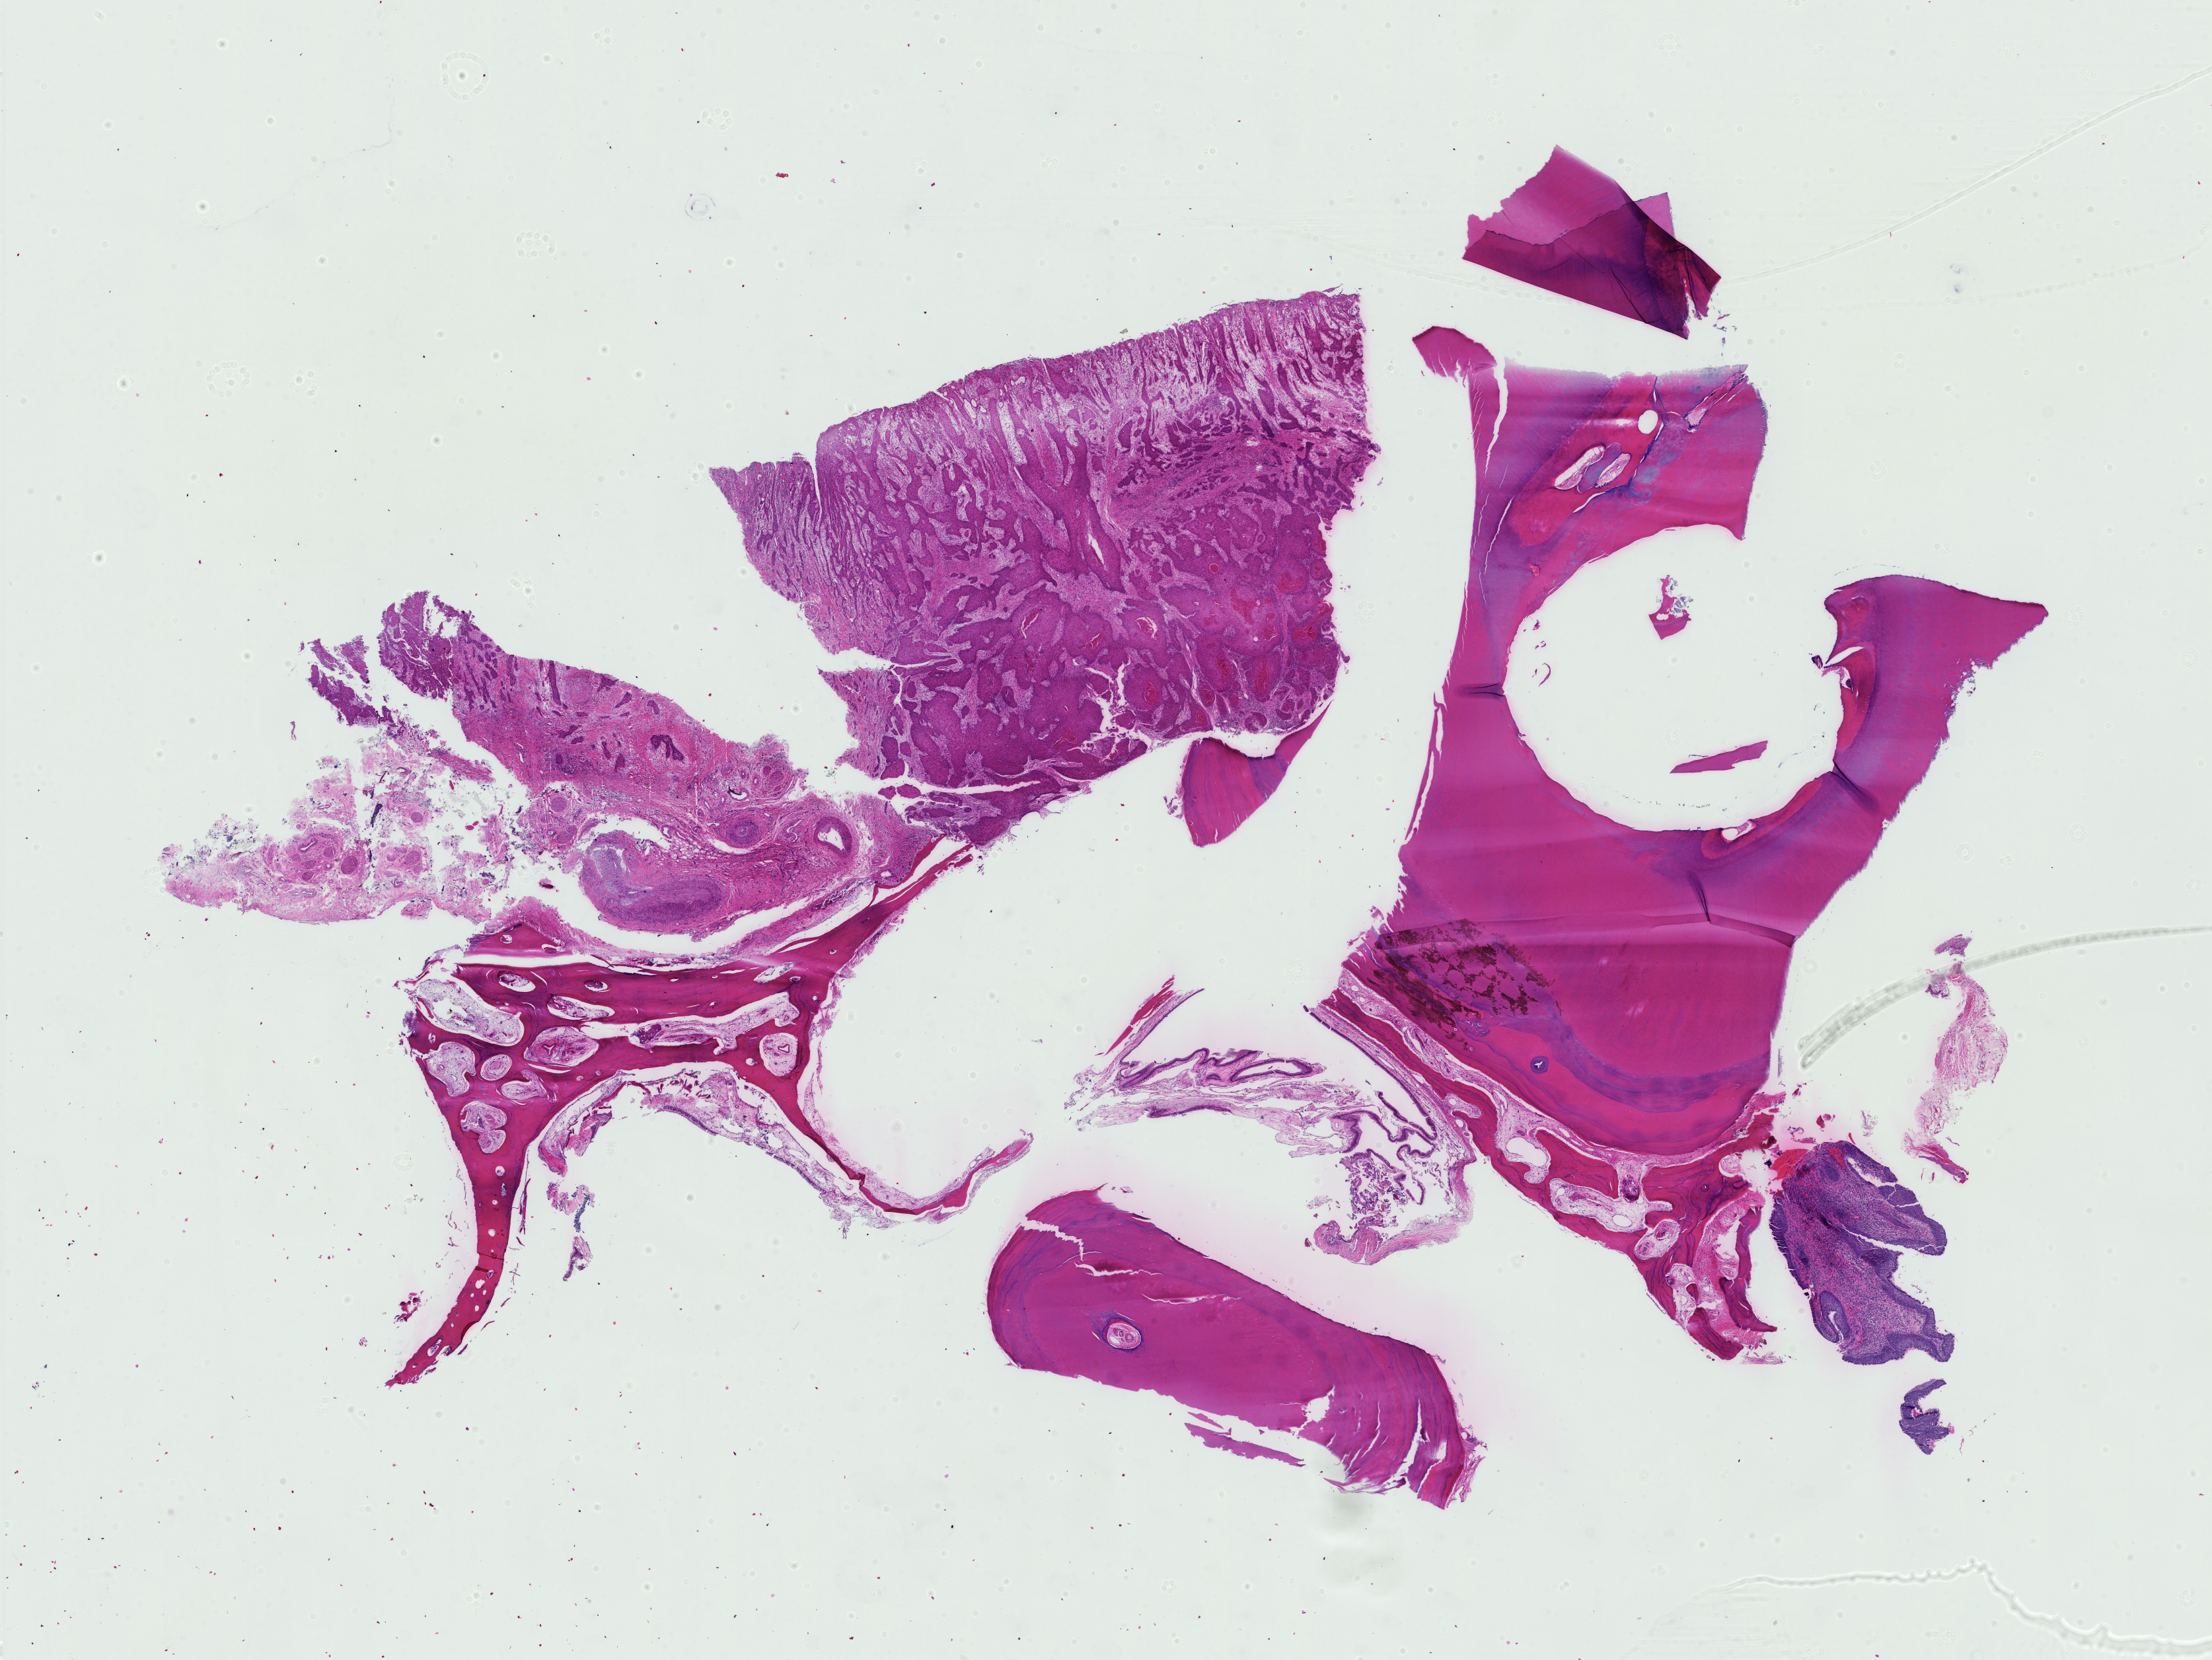
Digitized Hematoxylin and eosin (H&E) stained tissue section (whole slide) — low-resolution overview of the scanned area, about 24.3 x 18.2 mm (acquisition: 40x scan), formalin-fixed paraffin-embedded (FFPE) diagnostic section, head and neck, primary tumour sample. Patient: female, age at initial diagnosis 79 years. Histologic grade: G1 (well differentiated).
Laterality: right. AJCC pathologic stage: IVA (7th edition). Diagnosis: Squamous cell carcinoma, NOS (floor of mouth, NOS).